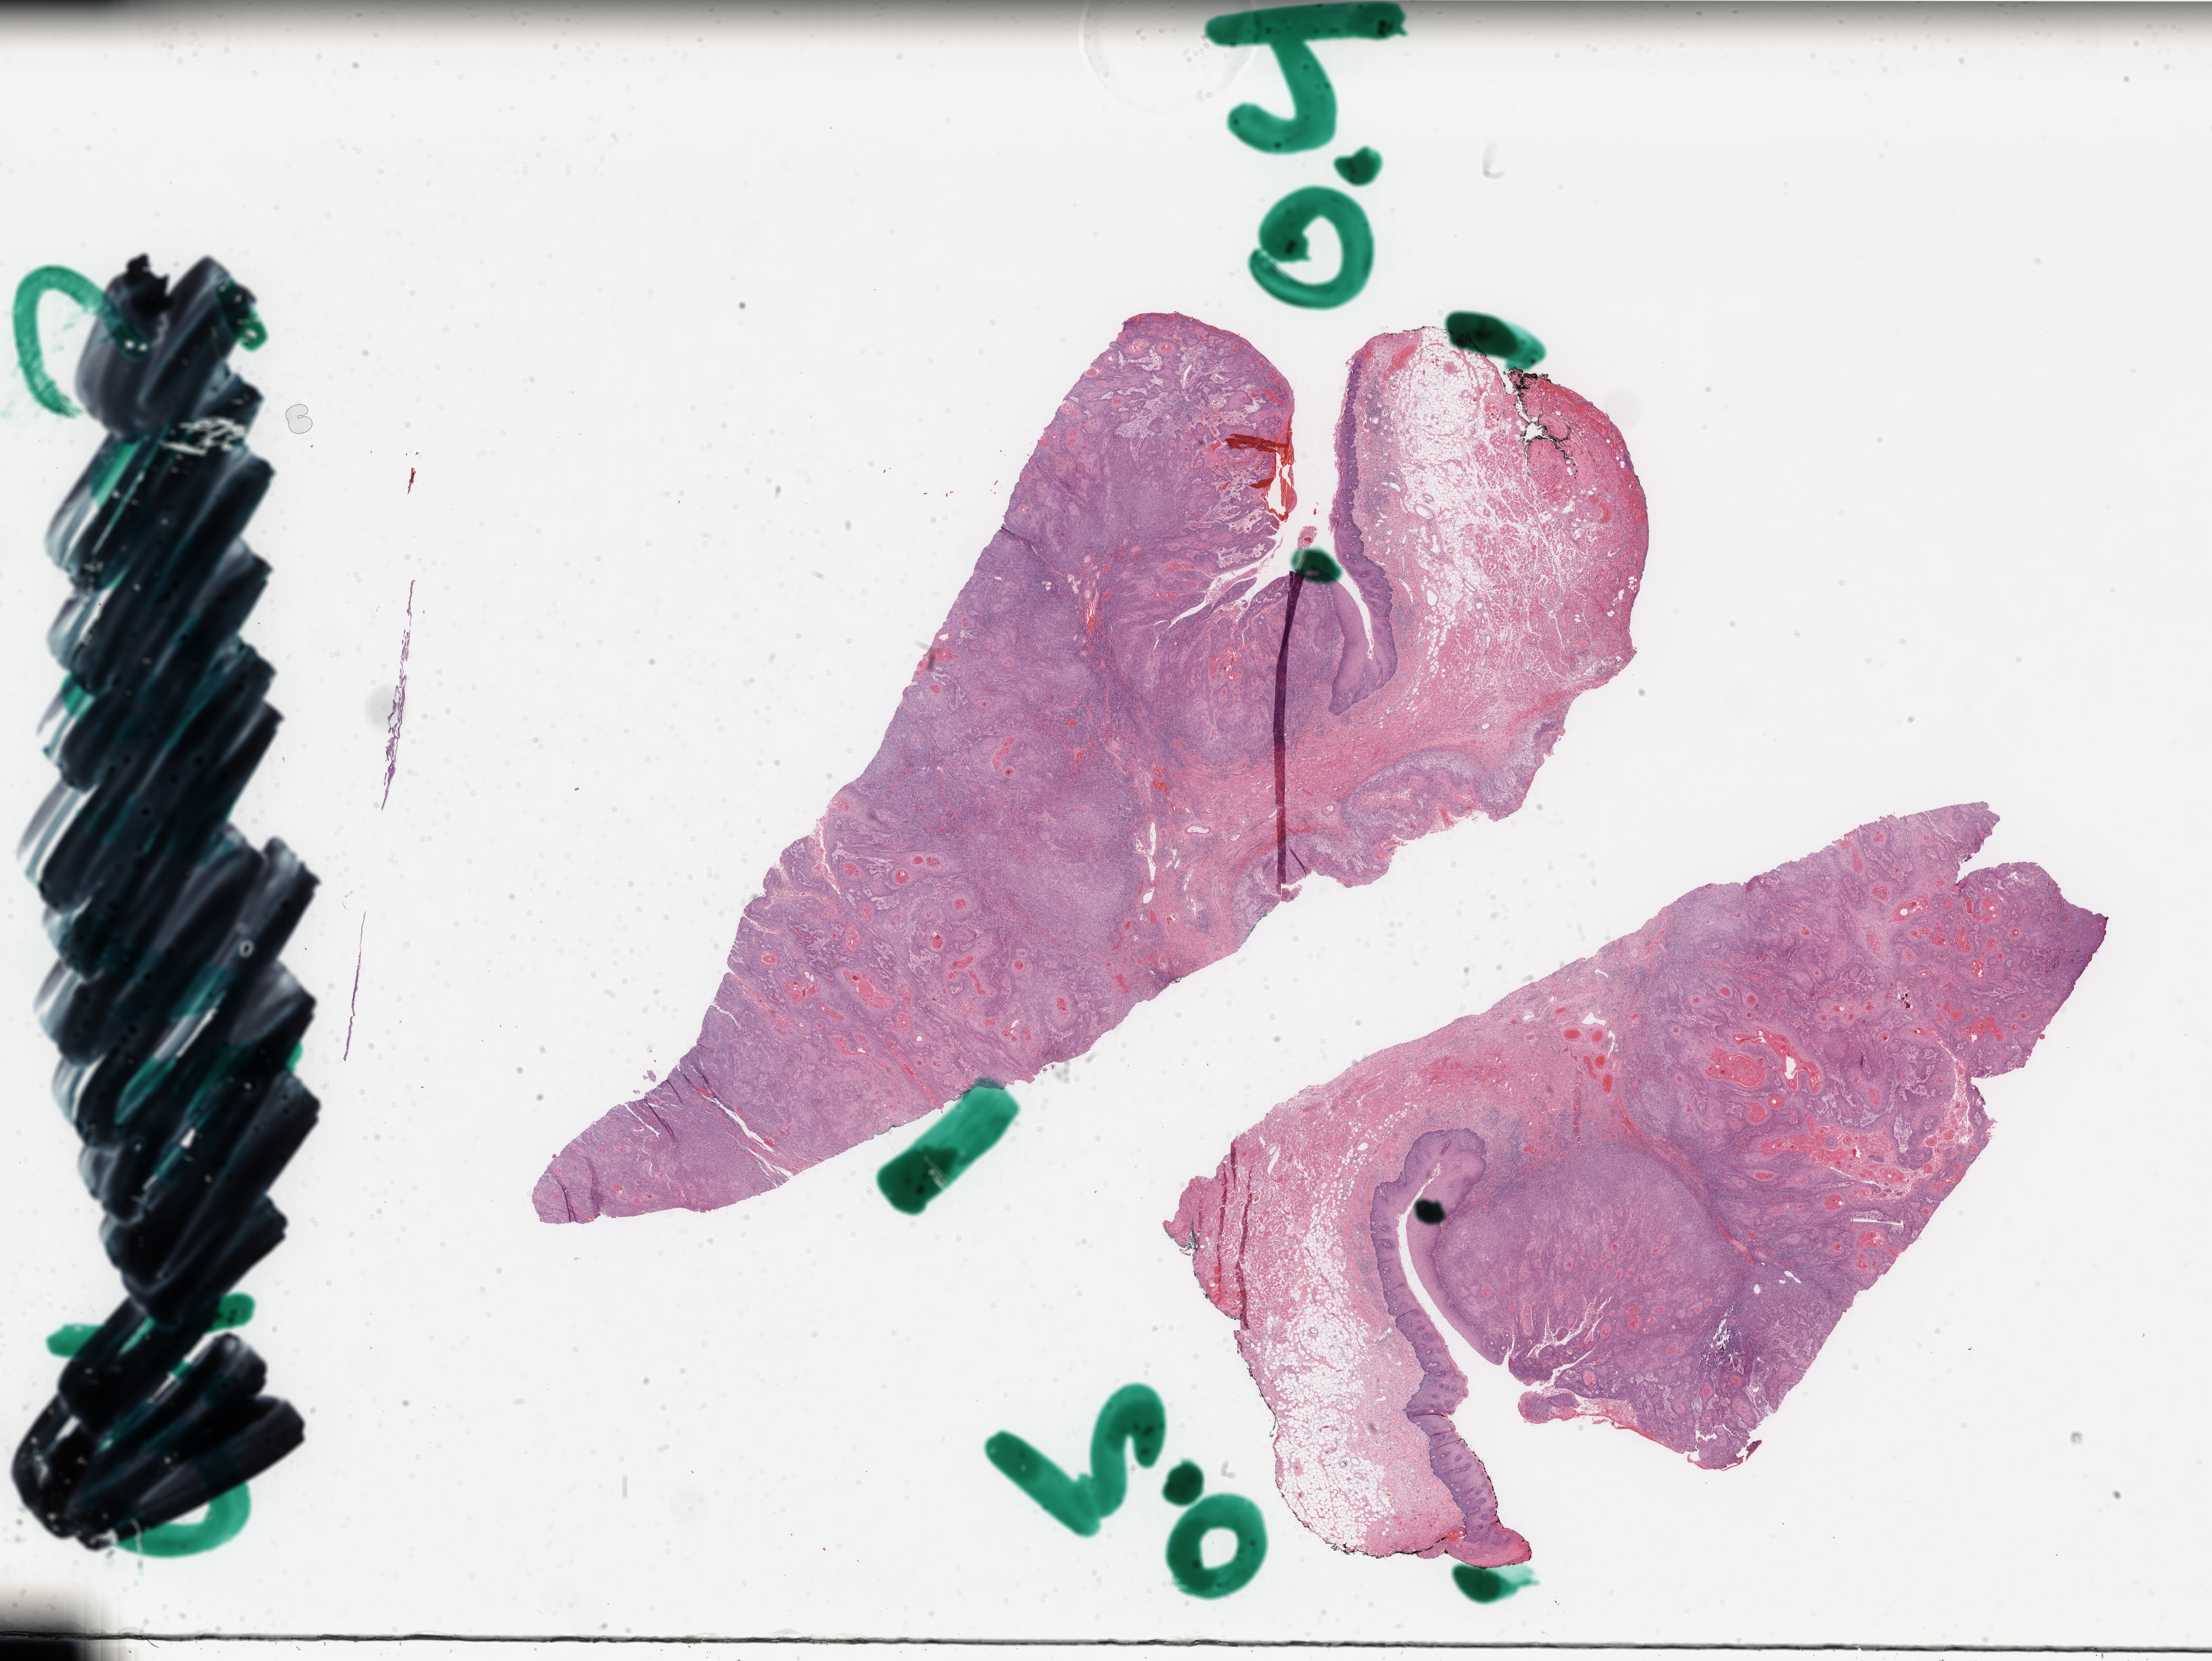
Whole-slide histology image, H&E, whole scanned area (about 31.8 x 23.9 mm, acquisition: 40x scan) shown as a low-resolution overview; FFPE section; primary tumour sample from the head and neck. Male patient; age at initial diagnosis 62 years. Histologic grade: G2 (moderately differentiated).
- AJCC pathologic stage: IVA (7th edition)
- lymph nodes positive (case pathology): 8 of 101 examined
- laterality: left
- pathologic diagnosis: Squamous cell carcinoma, keratinizing, NOS (gum, NOS)